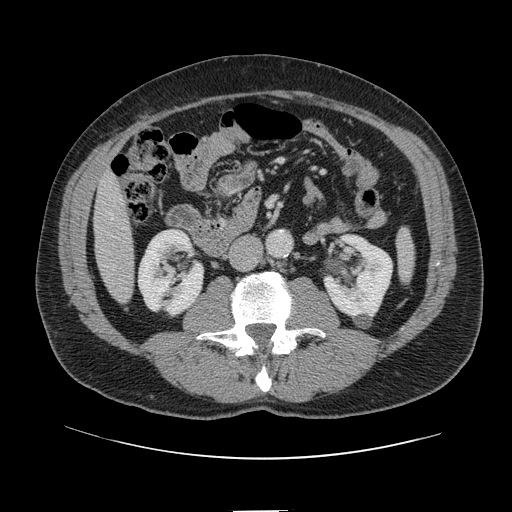
Contrast-enhanced abdominal CT, one axial slice; slice 22 of 161 in the series (ordered by position); 120 kVp; soft-tissue window (W 400 / L 40 HU); 2.5 mm slice thickness; 512 × 512 image matrix, field of view 412 × 412 mm. Male patient, age 66 years. From the clinical record (not read from this slice): diagnosis: colorectal cancer liver metastases, imaged before liver resection; multiple liver metastases: no; largest metastasis: 3.5 cm; disease in both lobes: no.
Outlined on this slice (expert manual segmentation):
- liver: bounding box <94,174,133,302> (left, top, right, bottom; pixels)
- planned liver remnant (the part of the liver to remain after resection): <94,174,130,253>